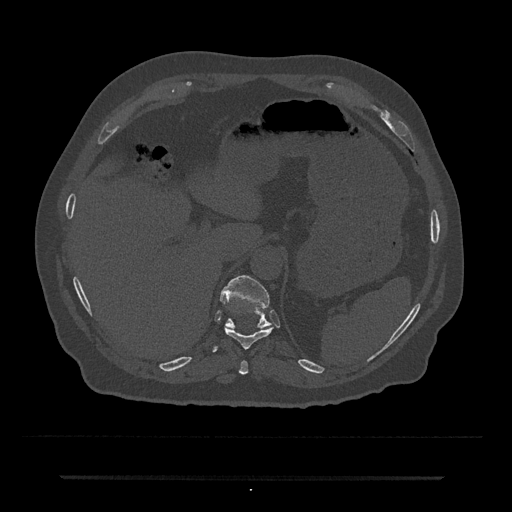
CT including the spine, one axial slice; slice 216 of 797 in the series (ordered by position); 120 kVp; bone window (W 1800 / L 400 HU); 0.5 mm slice thickness; 512 × 512 image matrix. Male patient, age 69 years. Case-level facts recorded for this patient, not image findings: primary cancer: prostate.
Outlined on this slice (semi-automatically segmented with operator editing):
- T10 vertebra: bounding box (x1, y1, x2, y2) in pixels: (212, 326, 274, 352)
- T11 vertebra: (220, 275, 271, 329)
- T9 vertebra: (239, 360, 249, 375)